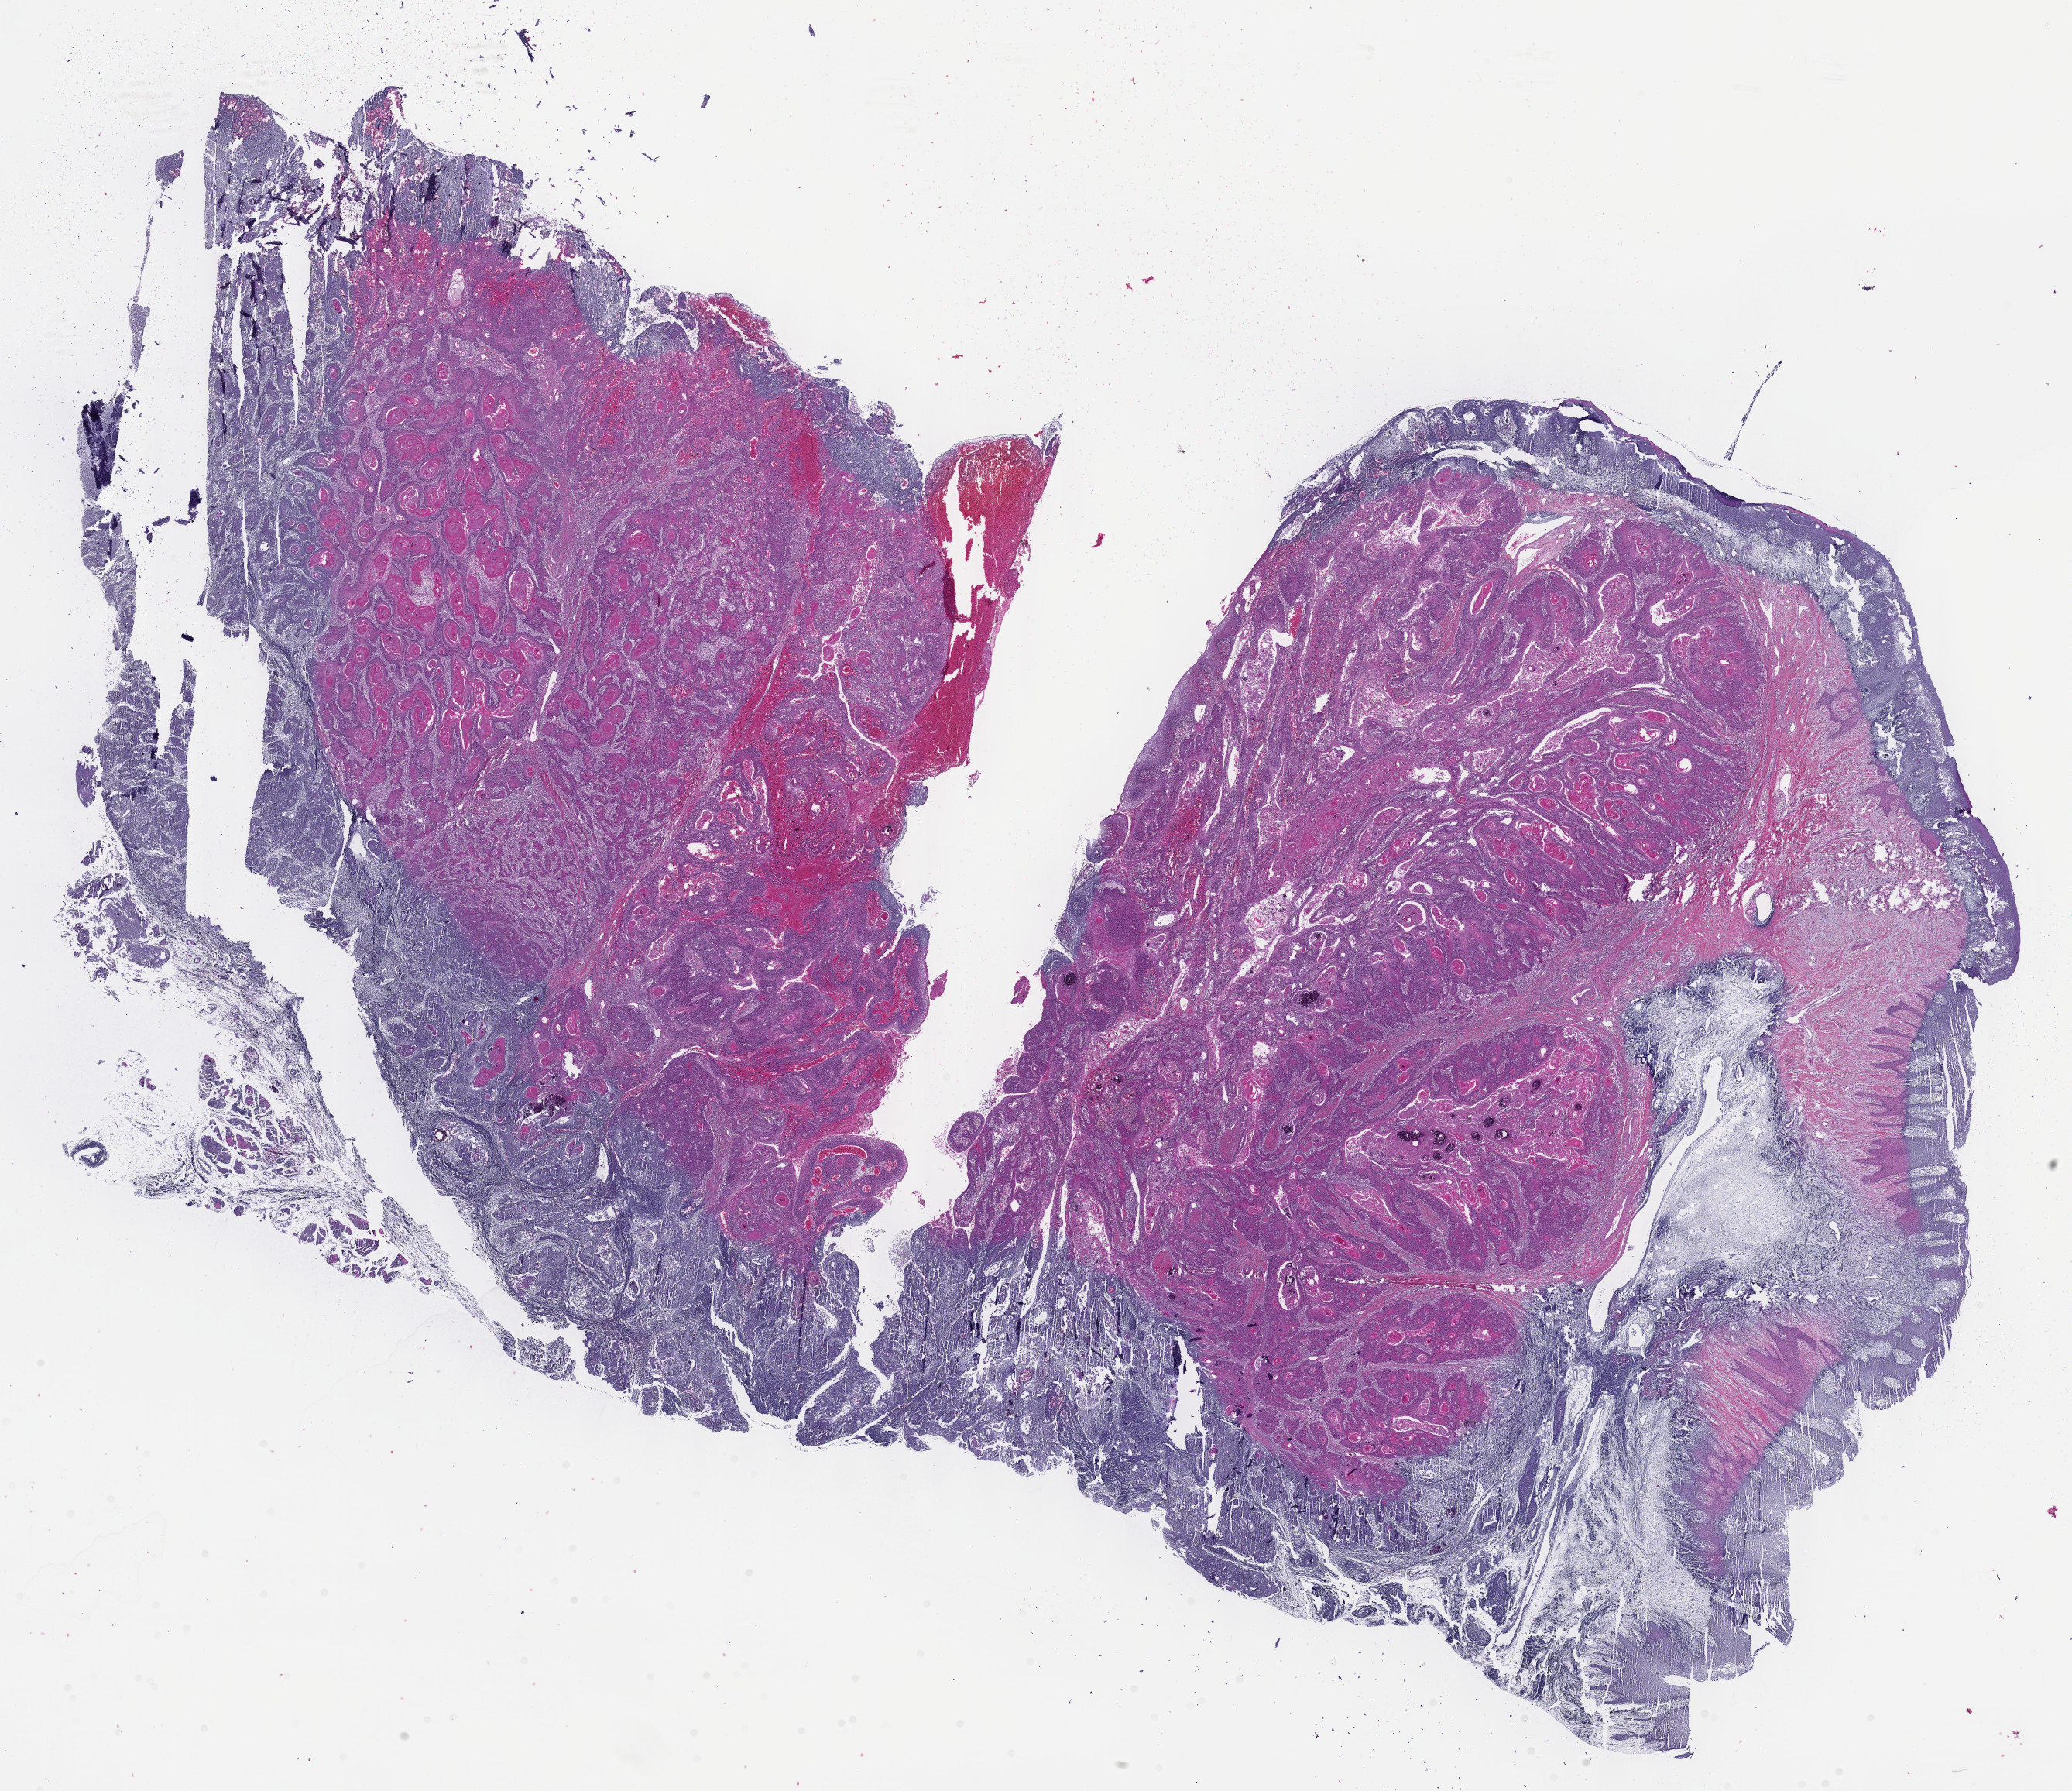
Digitized H&E-stained tissue section (whole slide), shown as a low-resolution overview of the whole scanned area (about 21.6 x 18.7 mm, from a 40x scan), formalin-fixed paraffin-embedded (FFPE) diagnostic section, head and neck, primary tumour sample. Male, age 47 years at initial diagnosis. Histologic grade: G2 (moderately differentiated).
AJCC pathologic stage: IVA (7th edition). TNM: T4a N2b. Lymph nodes positive (case pathology): 2 of 10 examined. Histologic diagnosis: Squamous cell carcinoma, NOS (overlapping lesion of lip, oral cavity and pharynx).